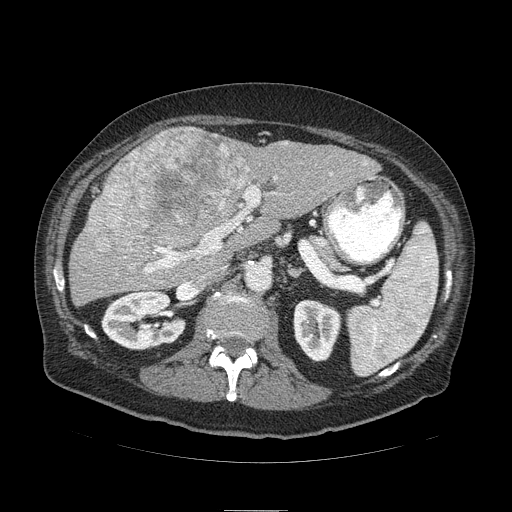
Contrast-enhanced abdominal CT (liver protocol), one axial slice. Position 48 of 103 along the scan axis. Reconstruction kernel STANDARD. 120 kVp. Soft-tissue window (W 400 / L 40 HU). 512 × 512 image matrix, field of view 440 × 440 mm. Case-level facts recorded for this patient, not image findings: diagnosis: hepatocellular carcinoma (patient treated with transarterial chemoembolisation; whether this scan precedes or follows treatment is not stated here); TNM stage (as recorded): Stage-IIIA; Child-Pugh class: B; tumour differentiation: well differentiated; tumour size: 13 cm.
Structures marked on this image (semi-automatically segmented with operator editing):
- liver parenchyma outside the tumour (the mass and vessels are separate outlines, so this box may not span the whole liver): bounding box <68,126,380,306> (left, top, right, bottom; pixels)
- mass: <86,128,255,269>
- liver vessels: <132,153,366,273>